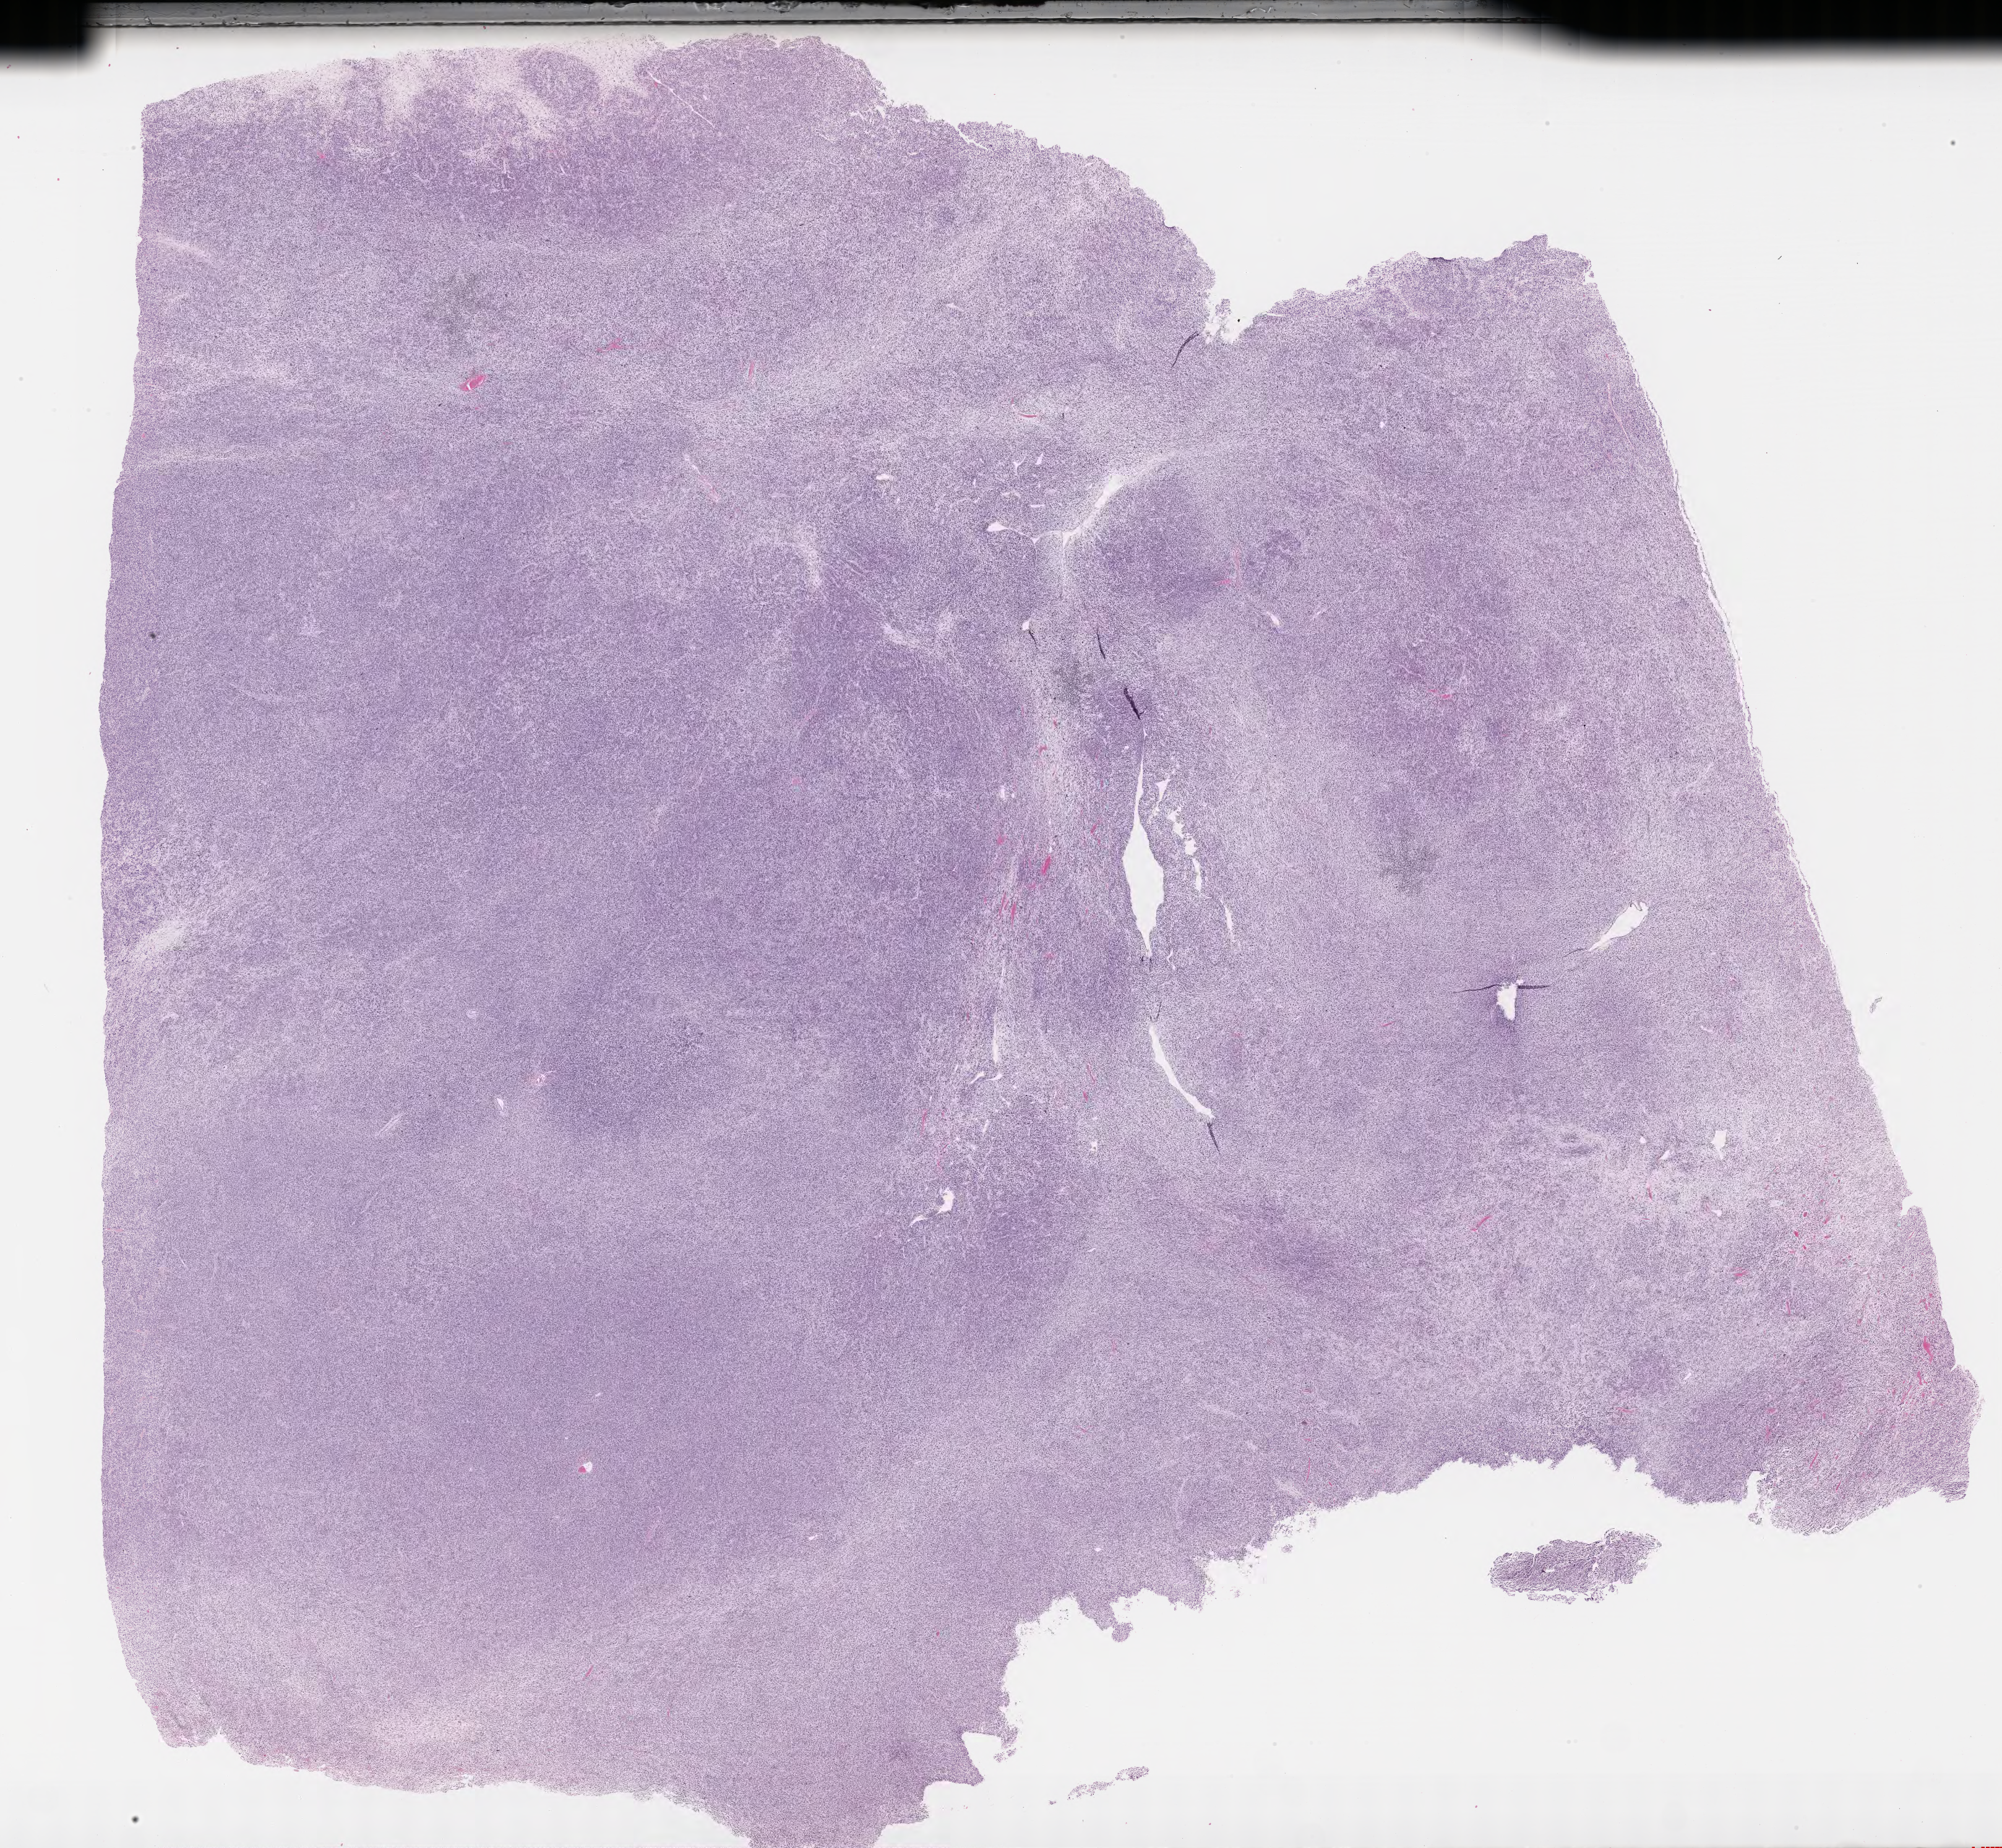
Digitized hematoxylin and eosin (H&E)-stained section of tumor tissue, whole scanned area (about 26.2 x 24.2 mm) shown as a low-resolution overview, formalin-fixed, paraffin-embedded (FFPE) tissue, site: testicle-left. Male patient, age at diagnosis 14.5 years.
Stage (as recorded): 1. Metastatic status at presentation (as recorded): non-metastatic (unconfirmed). Diagnosis: rhabdomyosarcoma; histological classification: embryonal rhabdomyosarcoma.